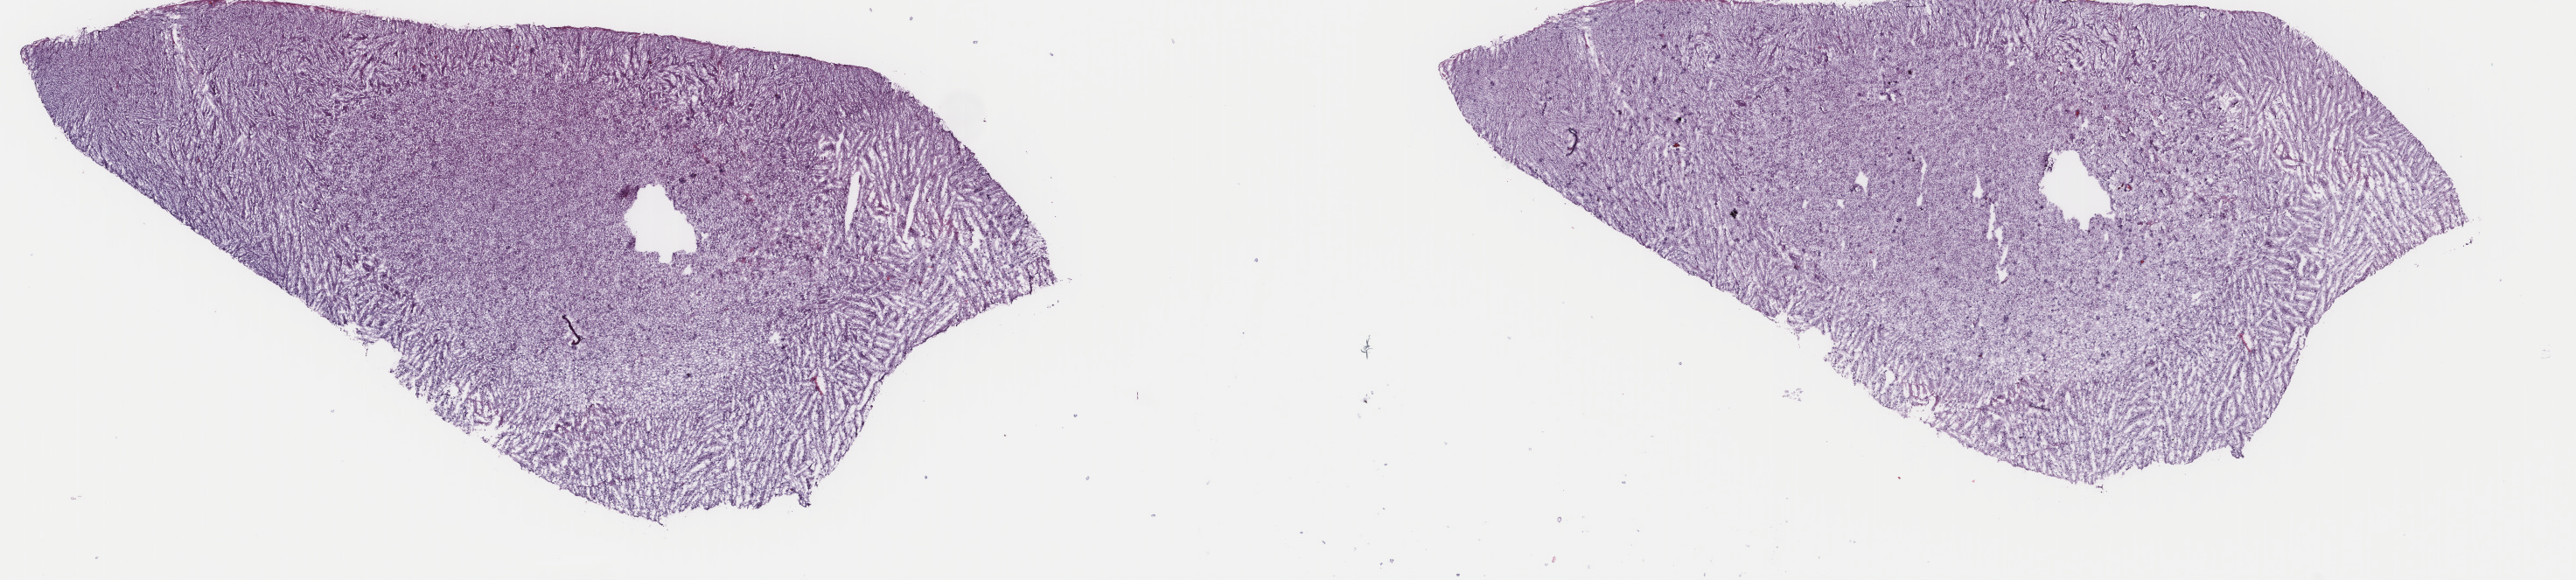
Whole-slide histology image, H&E-stained — low-resolution overview of the scanned area, about 23.4 x 5.3 mm (acquisition: 40x scan), frozen section, sample: primary tumour, brain. Female patient; age at initial diagnosis 73 years. Histologic grade: G2 (moderately differentiated). Pathologist review of this section (percent, as recorded): tumour cells 40%, tumour nuclei 80%, normal cells 10%, stromal cells 50%, necrosis 0%. Inflammatory infiltration, as recorded: lymphocyte infiltration 0%, monocyte infiltration 0%, neutrophil infiltration 0%.
- diagnosis: Oligodendroglioma, NOS (cerebrum)